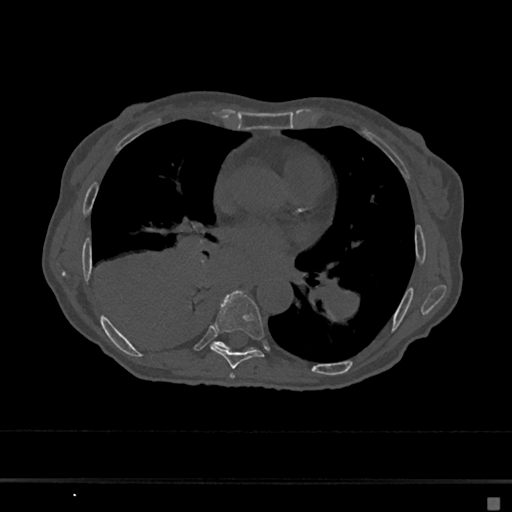
CT including the spine, one axial slice; slice 361 of 797 in the series (ordered by position); 120 kVp; bone window (W 1800 / L 400 HU); 0.5 mm slice thickness; 512 × 512 image matrix, field of view 360 × 360 mm. Female patient, age 68 years. From the clinical record (not read from this slice): primary cancer: renal.
Outlined on this slice (semi-automatic segmentation, software-assisted and operator-edited):
- T6 vertebra: bounding box [x1, y1, x2, y2] px = [229, 373, 235, 379]
- T7 vertebra: [210, 291, 264, 369]
- T8 vertebra: [215, 341, 254, 350]